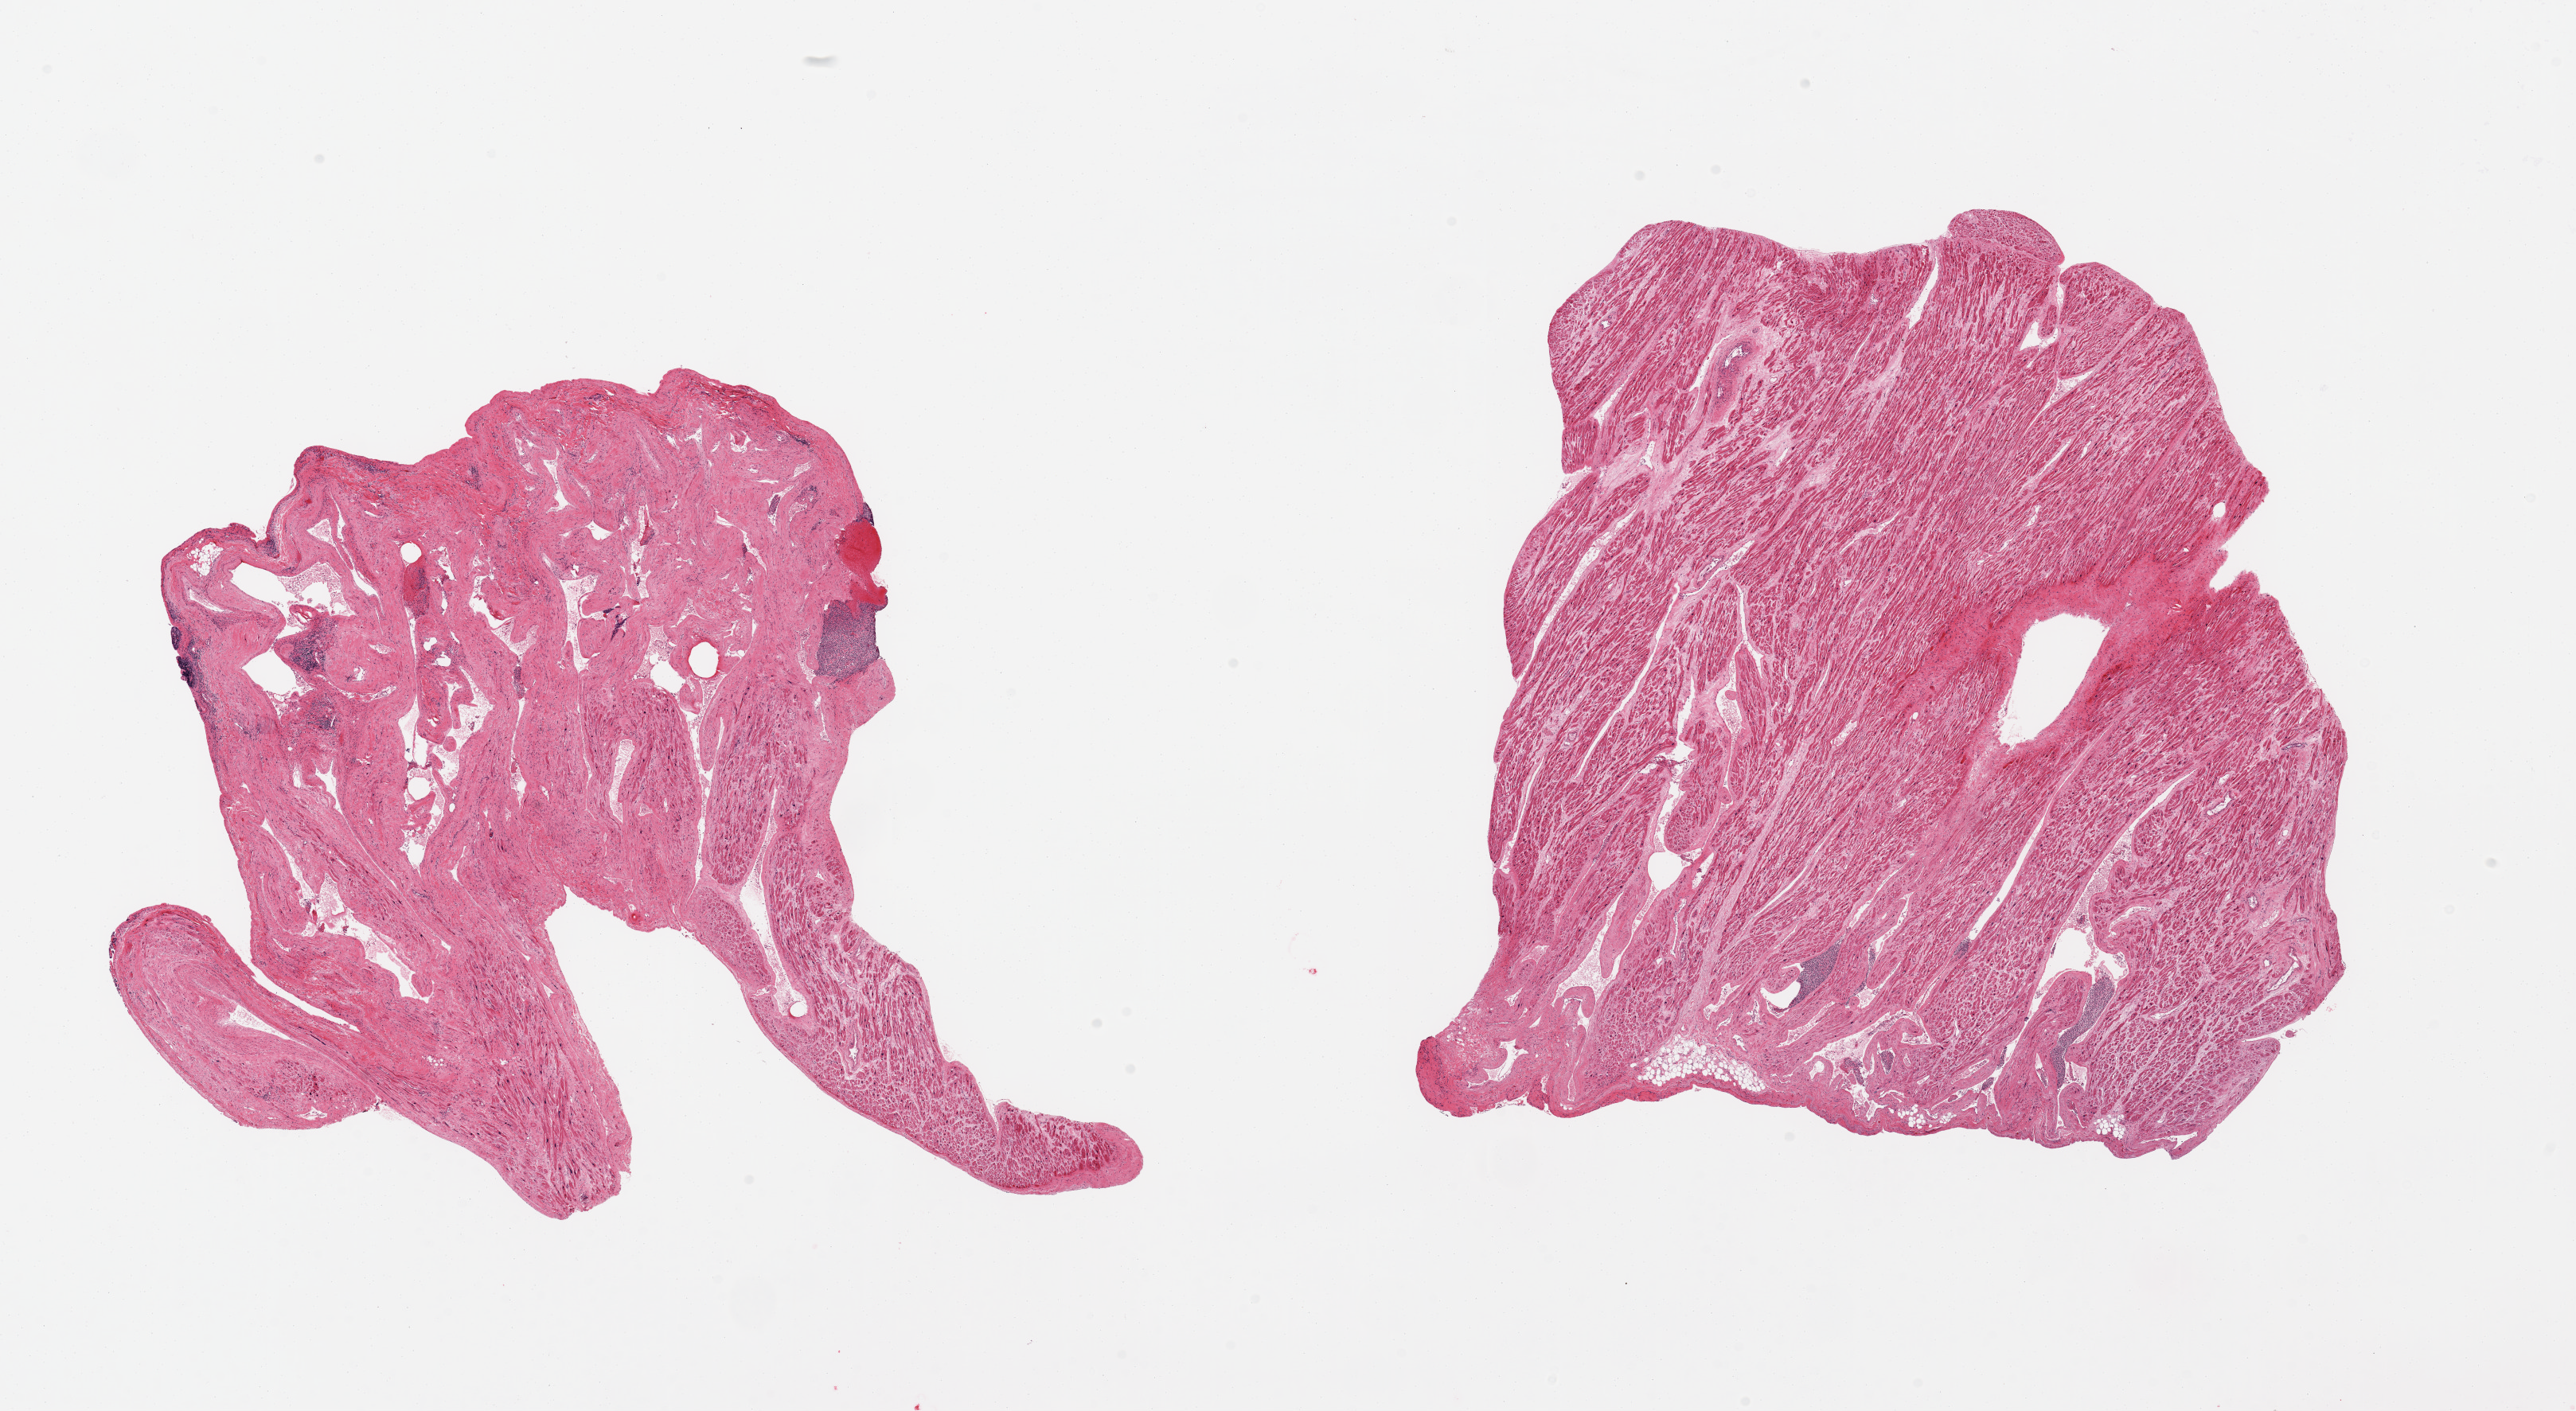
Digitized hematoxylin and eosin (H&E)-stained section, brightfield, whole scanned area (about 25.6 x 14.0 mm, acquisition: 20x scan) shown as a low-resolution overview, PAXgene-fixed paraffin-embedded (PFPE) section, section of auricular appendage (target tissue), tissue donor sample. Male donor.
Pathologist's review note for this sample: 2 pieces, acute inflammatory microaggregates, unknown significance.